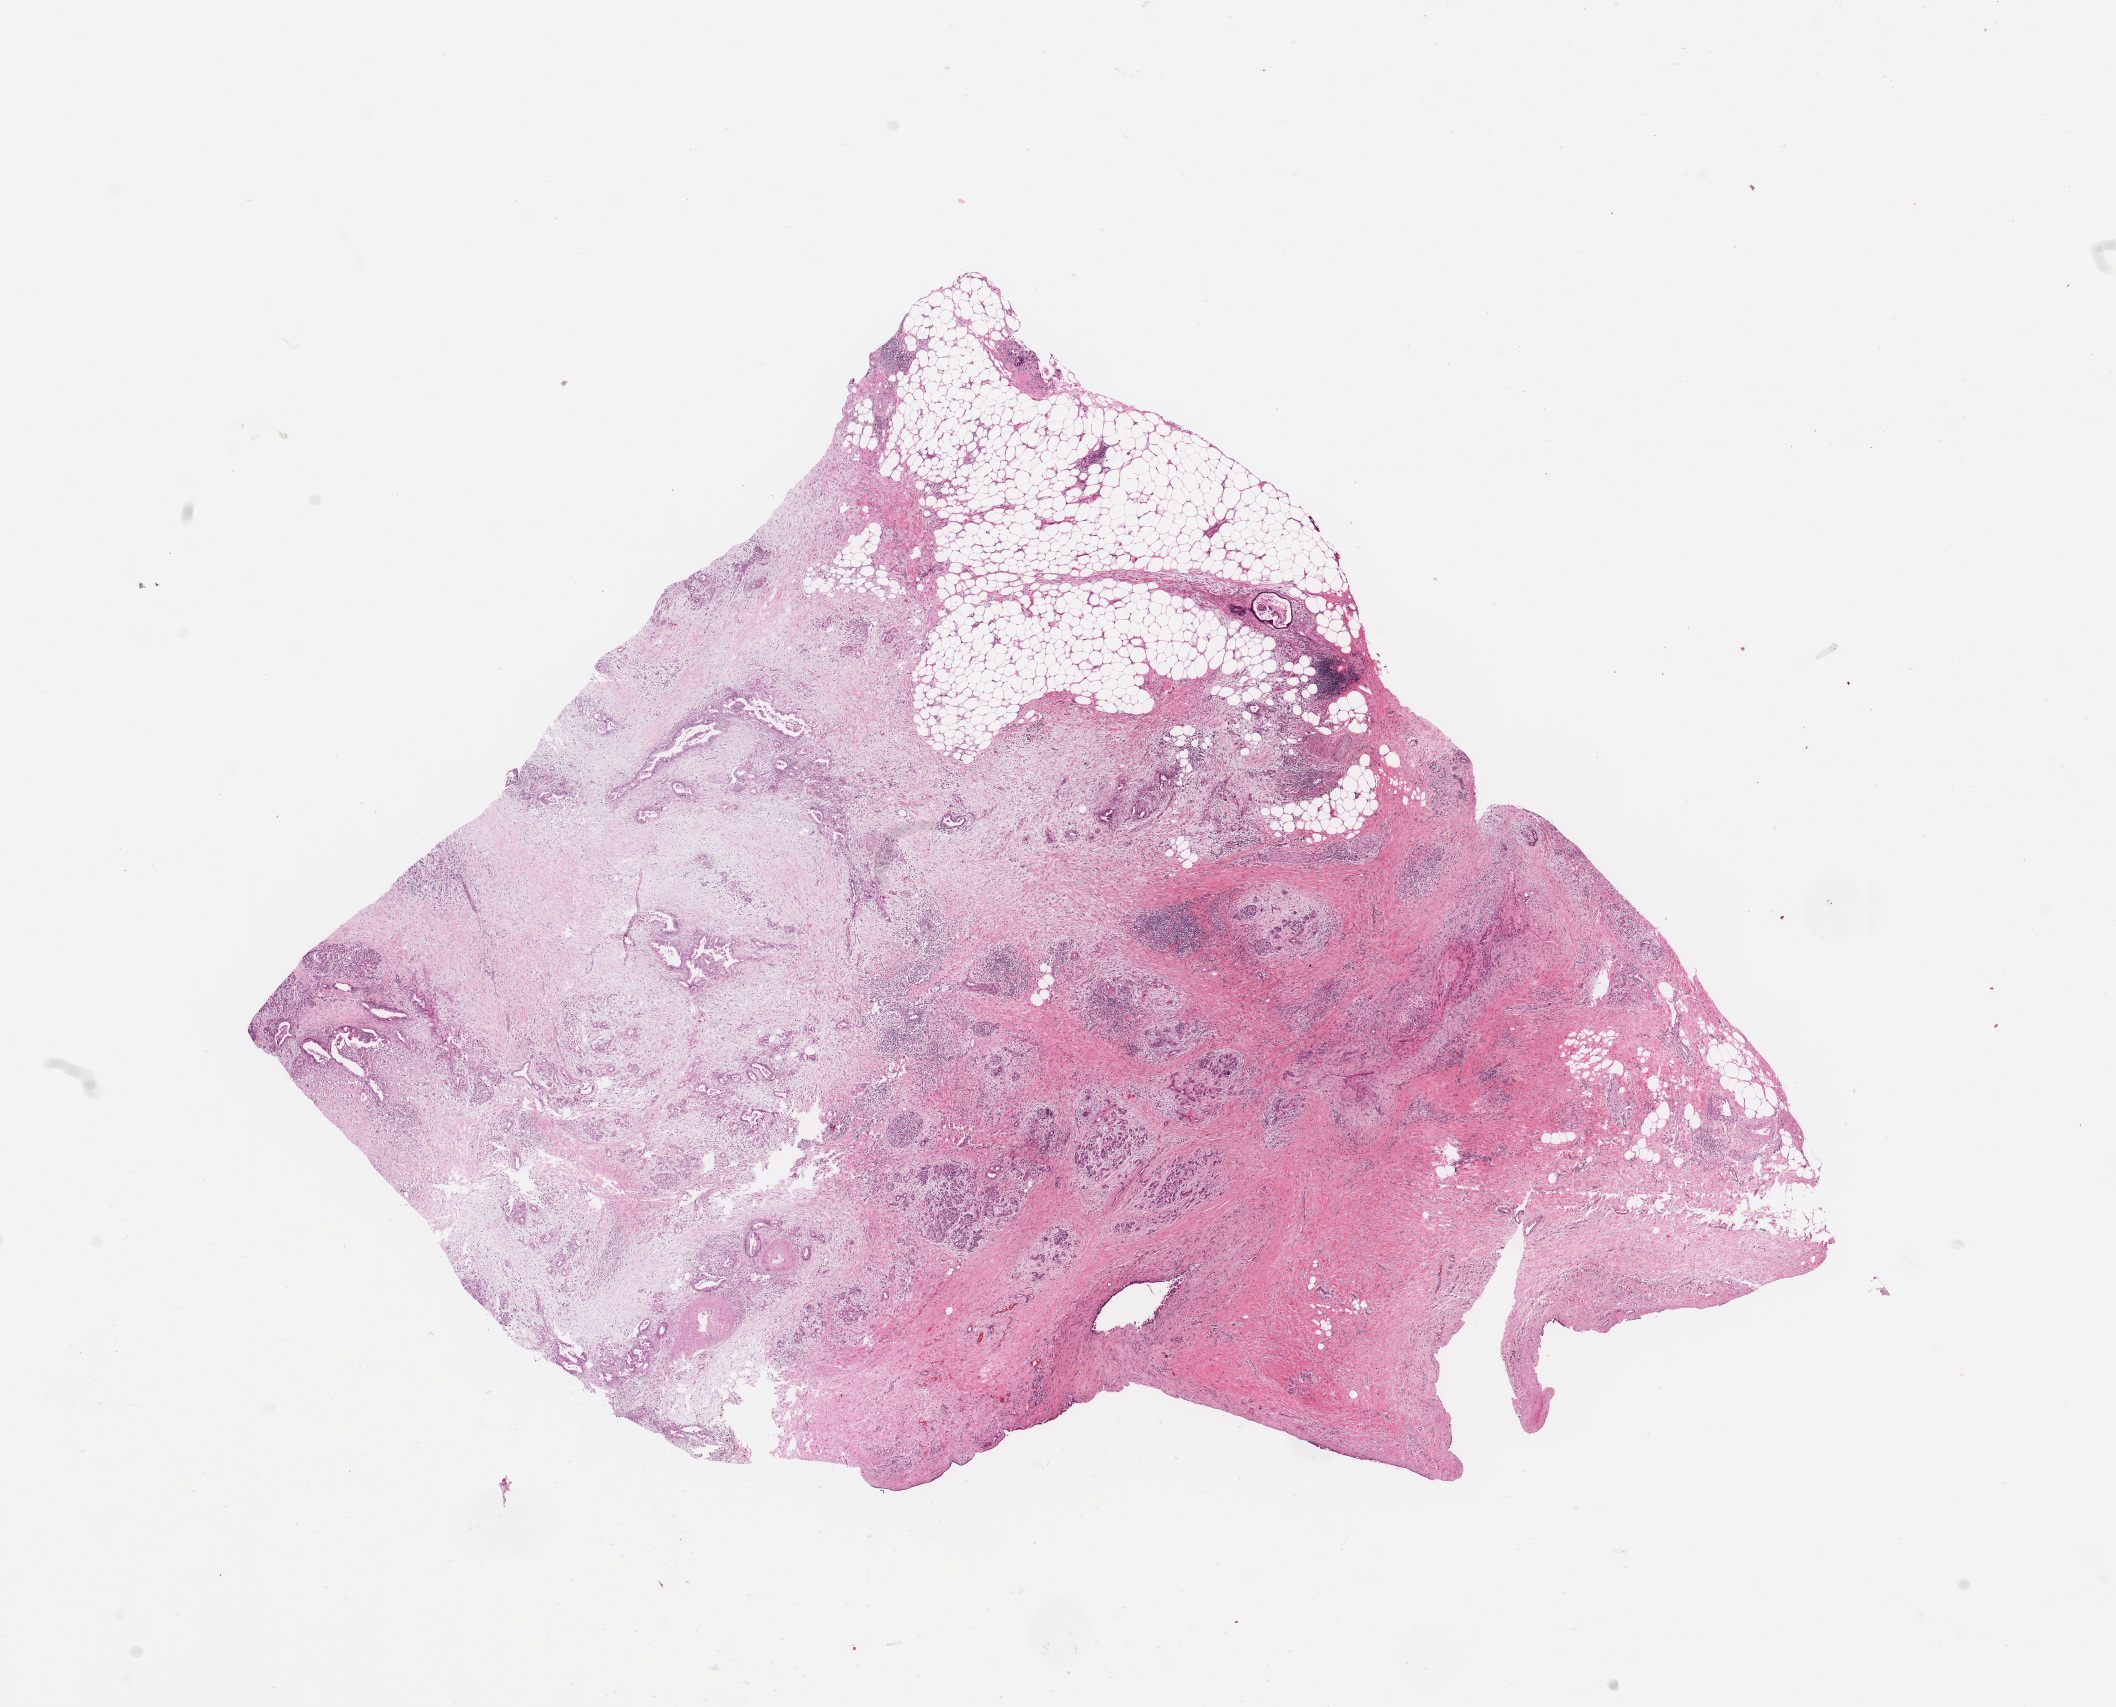
Hematoxylin and eosin (H&E) stained whole-slide image — low-resolution overview of the scanned area, about 16.7 x 13.5 mm, pancreas, tumour tissue. 76-year-old female patient.
Diagnosis: Infiltrating duct carcinoma, NOS.